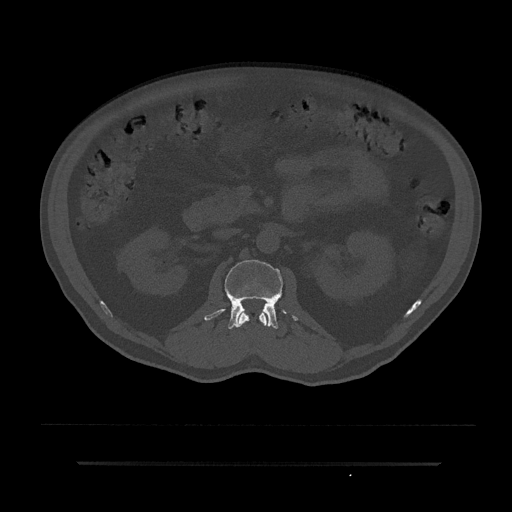
CT including the spine, one axial slice; position 97 of 797 along the scan axis; reconstruction kernel Br40s/3; bone window (W 1800 / L 400 HU); 512 × 512 image matrix, field of view 464 × 464 mm. Patient: male, 59 years. From the clinical record (not read from this slice): primary cancer: bile ducts.
Outlined on this slice (semi-automatically segmented with operator editing):
- L1 vertebra: bounding box <237,311,267,327> (left, top, right, bottom; pixels)
- L2 vertebra: <204,260,298,329>